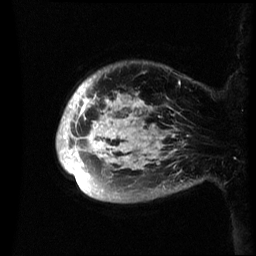
Breast MRI (dynamic contrast-enhanced), one sagittal slice. Slice 6 of 60 in the series (ordered by position). Dynamic contrast-enhanced series, image 2 of 3 at this slice position (ordered by acquisition). 1.5 T. TE 4.2 ms, TR 8.4 ms. 256 × 256 image matrix. Female patient, age 48 years.
Outlined on this slice (semi-automatic segmentation, software-assisted and operator-edited):
- analysis volume of interest (the breast-tissue region the enhancement analysis was run in; not a lesion): bounding box [x1, y1, x2, y2] px = [56, 66, 193, 203]
- tumour enhancement mask (voxels above the 70 % enhancement threshold inside the analysis volume of interest): [56, 83, 176, 184]